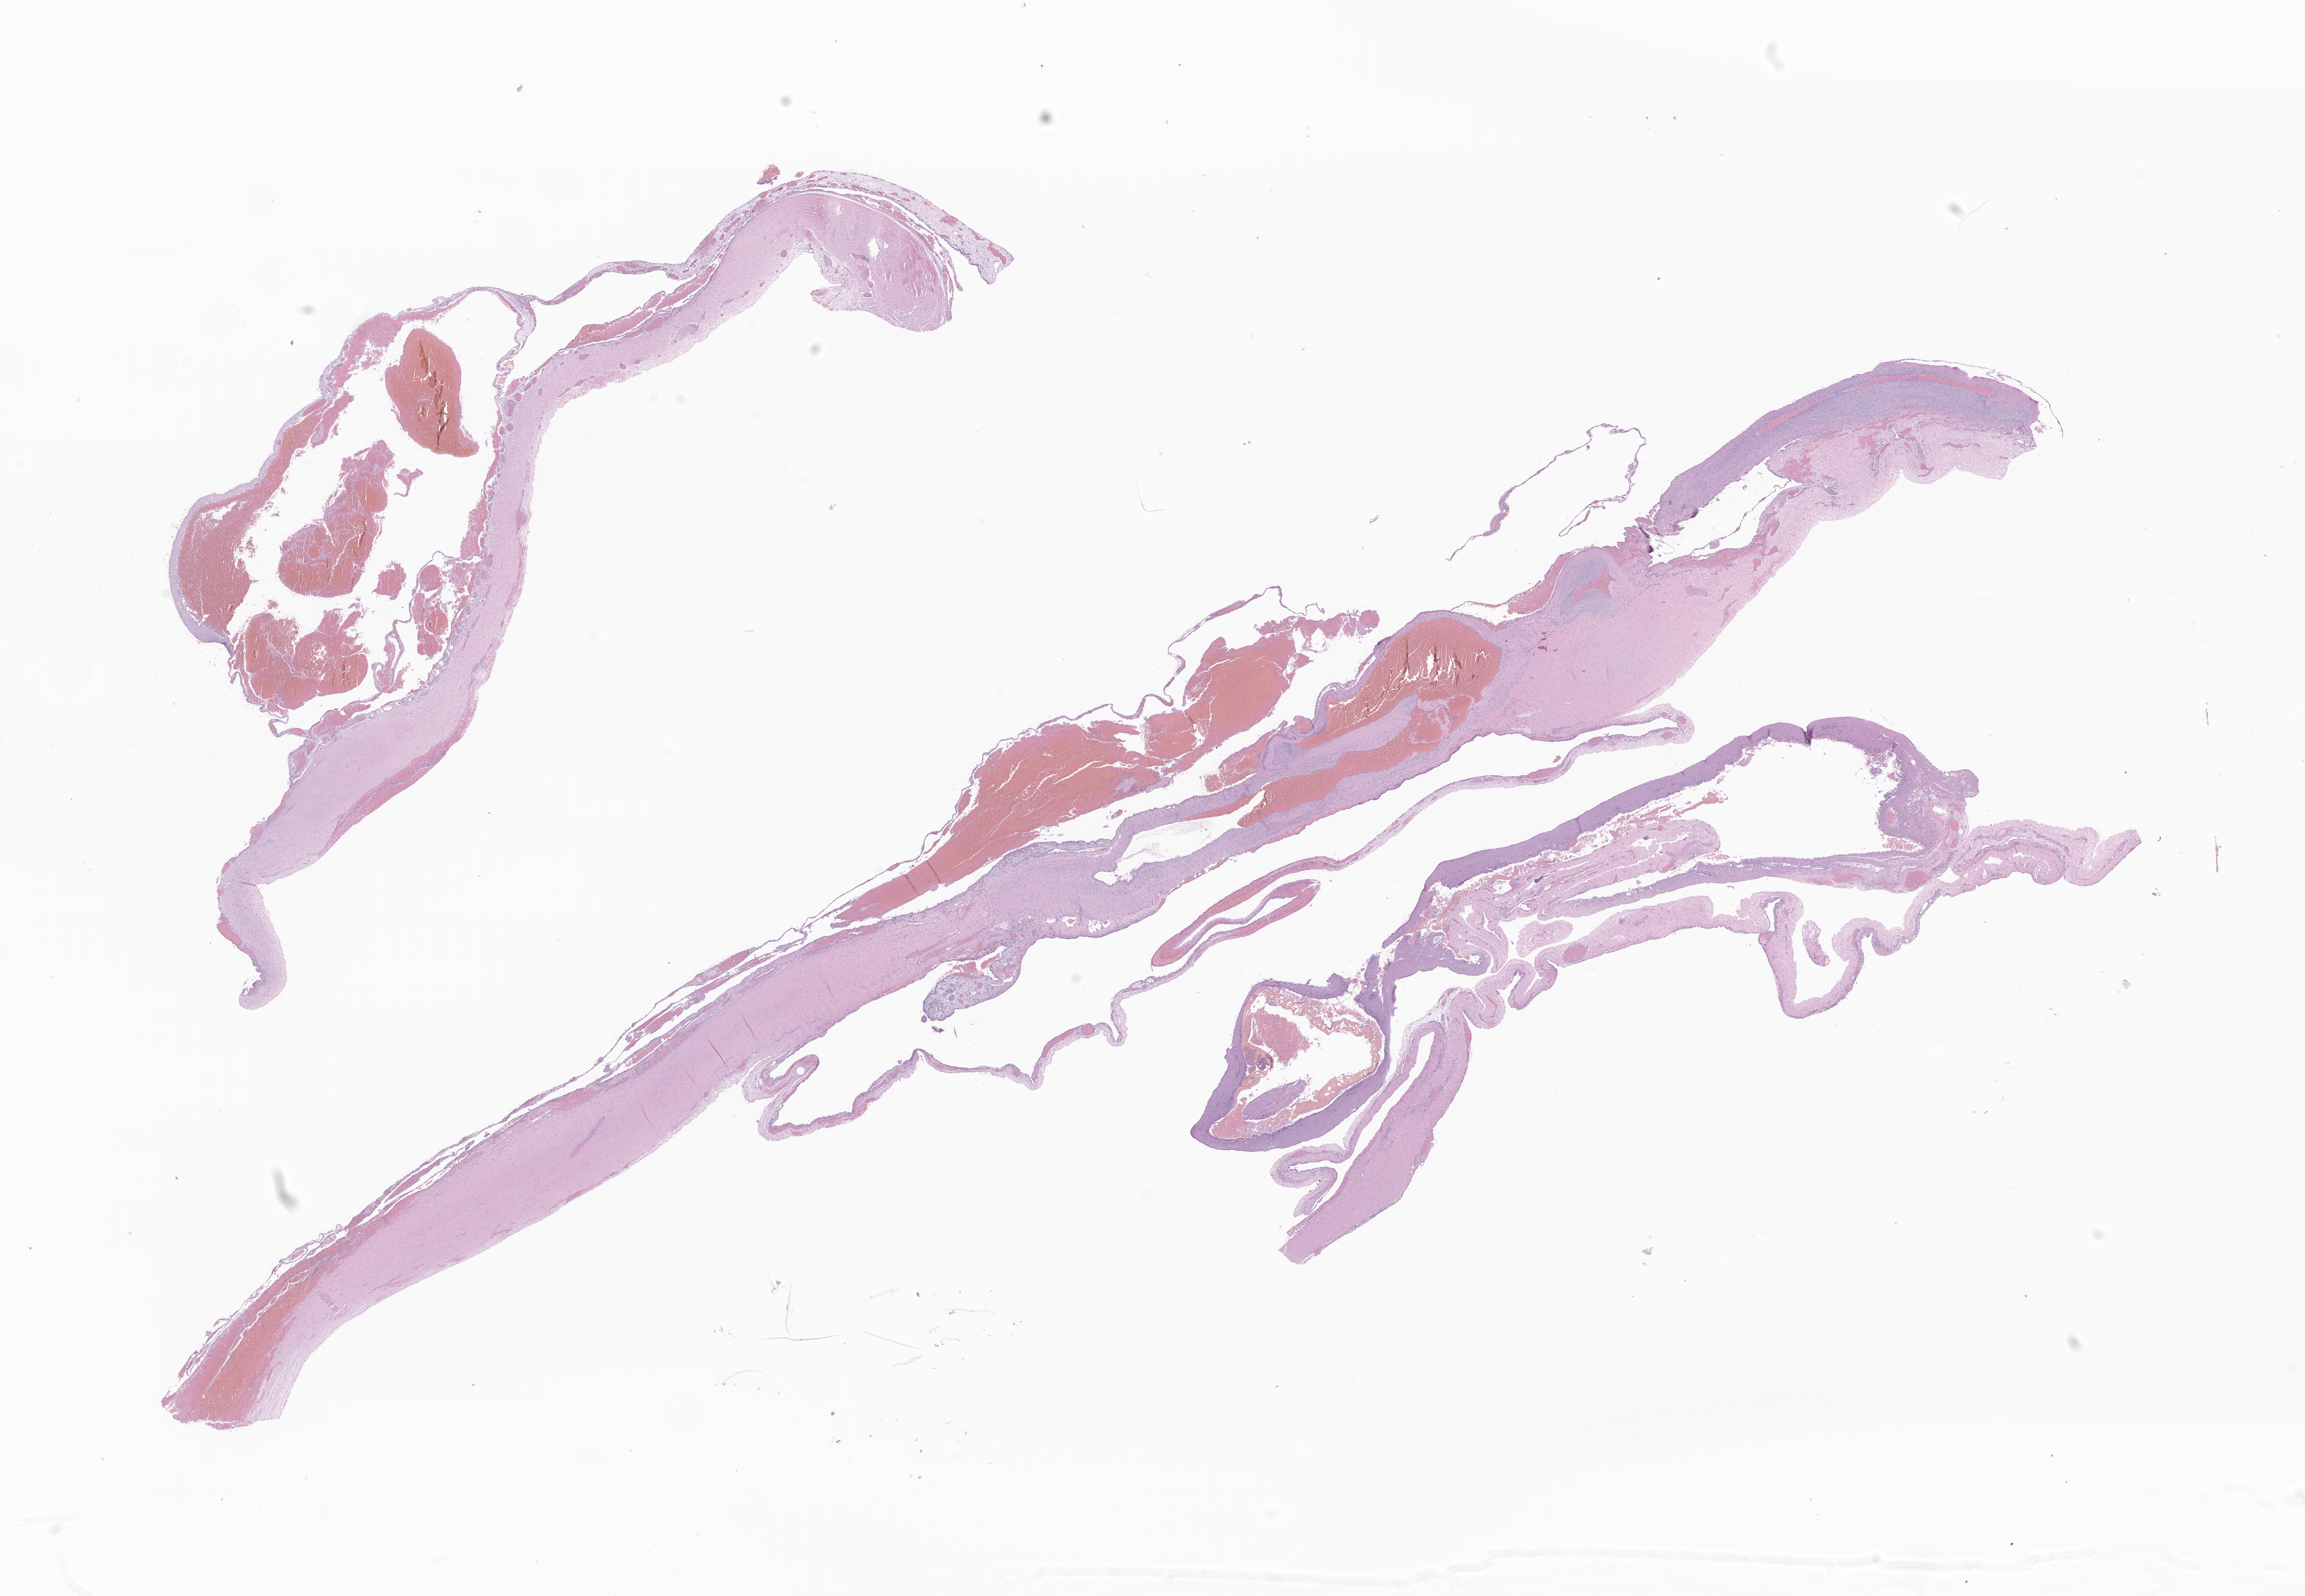
H&E whole-slide image of tumor tissue from the upper lobe of lung — a low-resolution overview of the entire scanned area, about 25.8 x 17.9 mm; FFPE section. Patient: male, age 37 months (3 years 1 month).
• recorded diagnosis: Pleuropulmonary blastoma